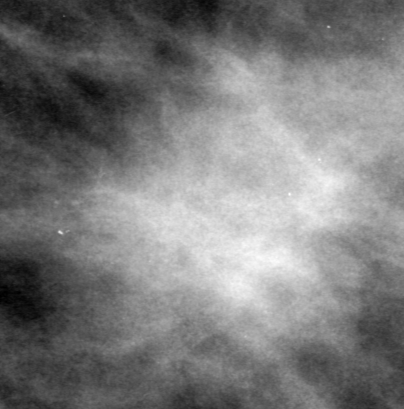
Cropped region of a digitized screen-film mammogram centred on a radiologist-marked abnormality; left breast; MLO view; BI-RADS breast density category 3 (scale 1–4).
Marked abnormality: mass, shape oval, margins microlobulated; BI-RADS assessment category 0 (incomplete: needs additional imaging); pathology (as recorded): malignant.